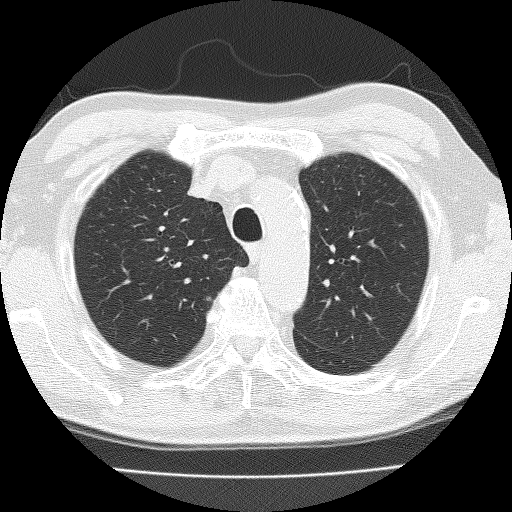
Low-dose screening chest CT, axial slice. Second screening round (one year after baseline). Lung window (W 1500 / L -600 HU). Slice 37 of 159 in the series. Male participant, aged 72 years at enrolment. Current smoker at enrolment.
- Lesion marked by an expert reader, box from (x=180, y=278) to (x=236, y=323) px.
- Screening reader's record for this exam: no non-calcified nodule ≥4 mm recorded.
- Lung cancer was diagnosed 396 days after this screen: squamous cell carcinoma, NOS, right upper lobe, moderately differentiated (G2), stage IIA (AJCC 6th edition), 25 mm at pathology.